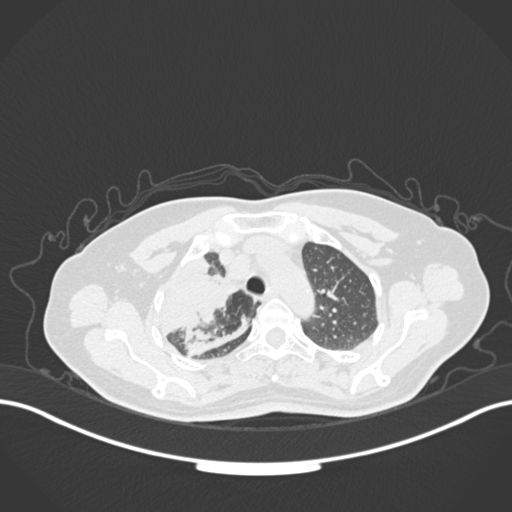
Chest CT, one axial slice. Position 126 of 177 along the scan axis. Reconstruction kernel B30f. 120 kVp. Lung window (W 1500 / L -600 HU). 1 mm slice thickness. 512 × 512 image matrix, field of view 400 × 400 mm. Female patient, age 60 years. From the clinical record (not read from this slice): clinical TNM (as recorded): T3 N1 M1.
Structures marked on this image (rectangle marked by the reading radiologist):
- lung tumour (recorded histology: adenocarcinoma): bounding box <152,249,243,341> (left, top, right, bottom; pixels)